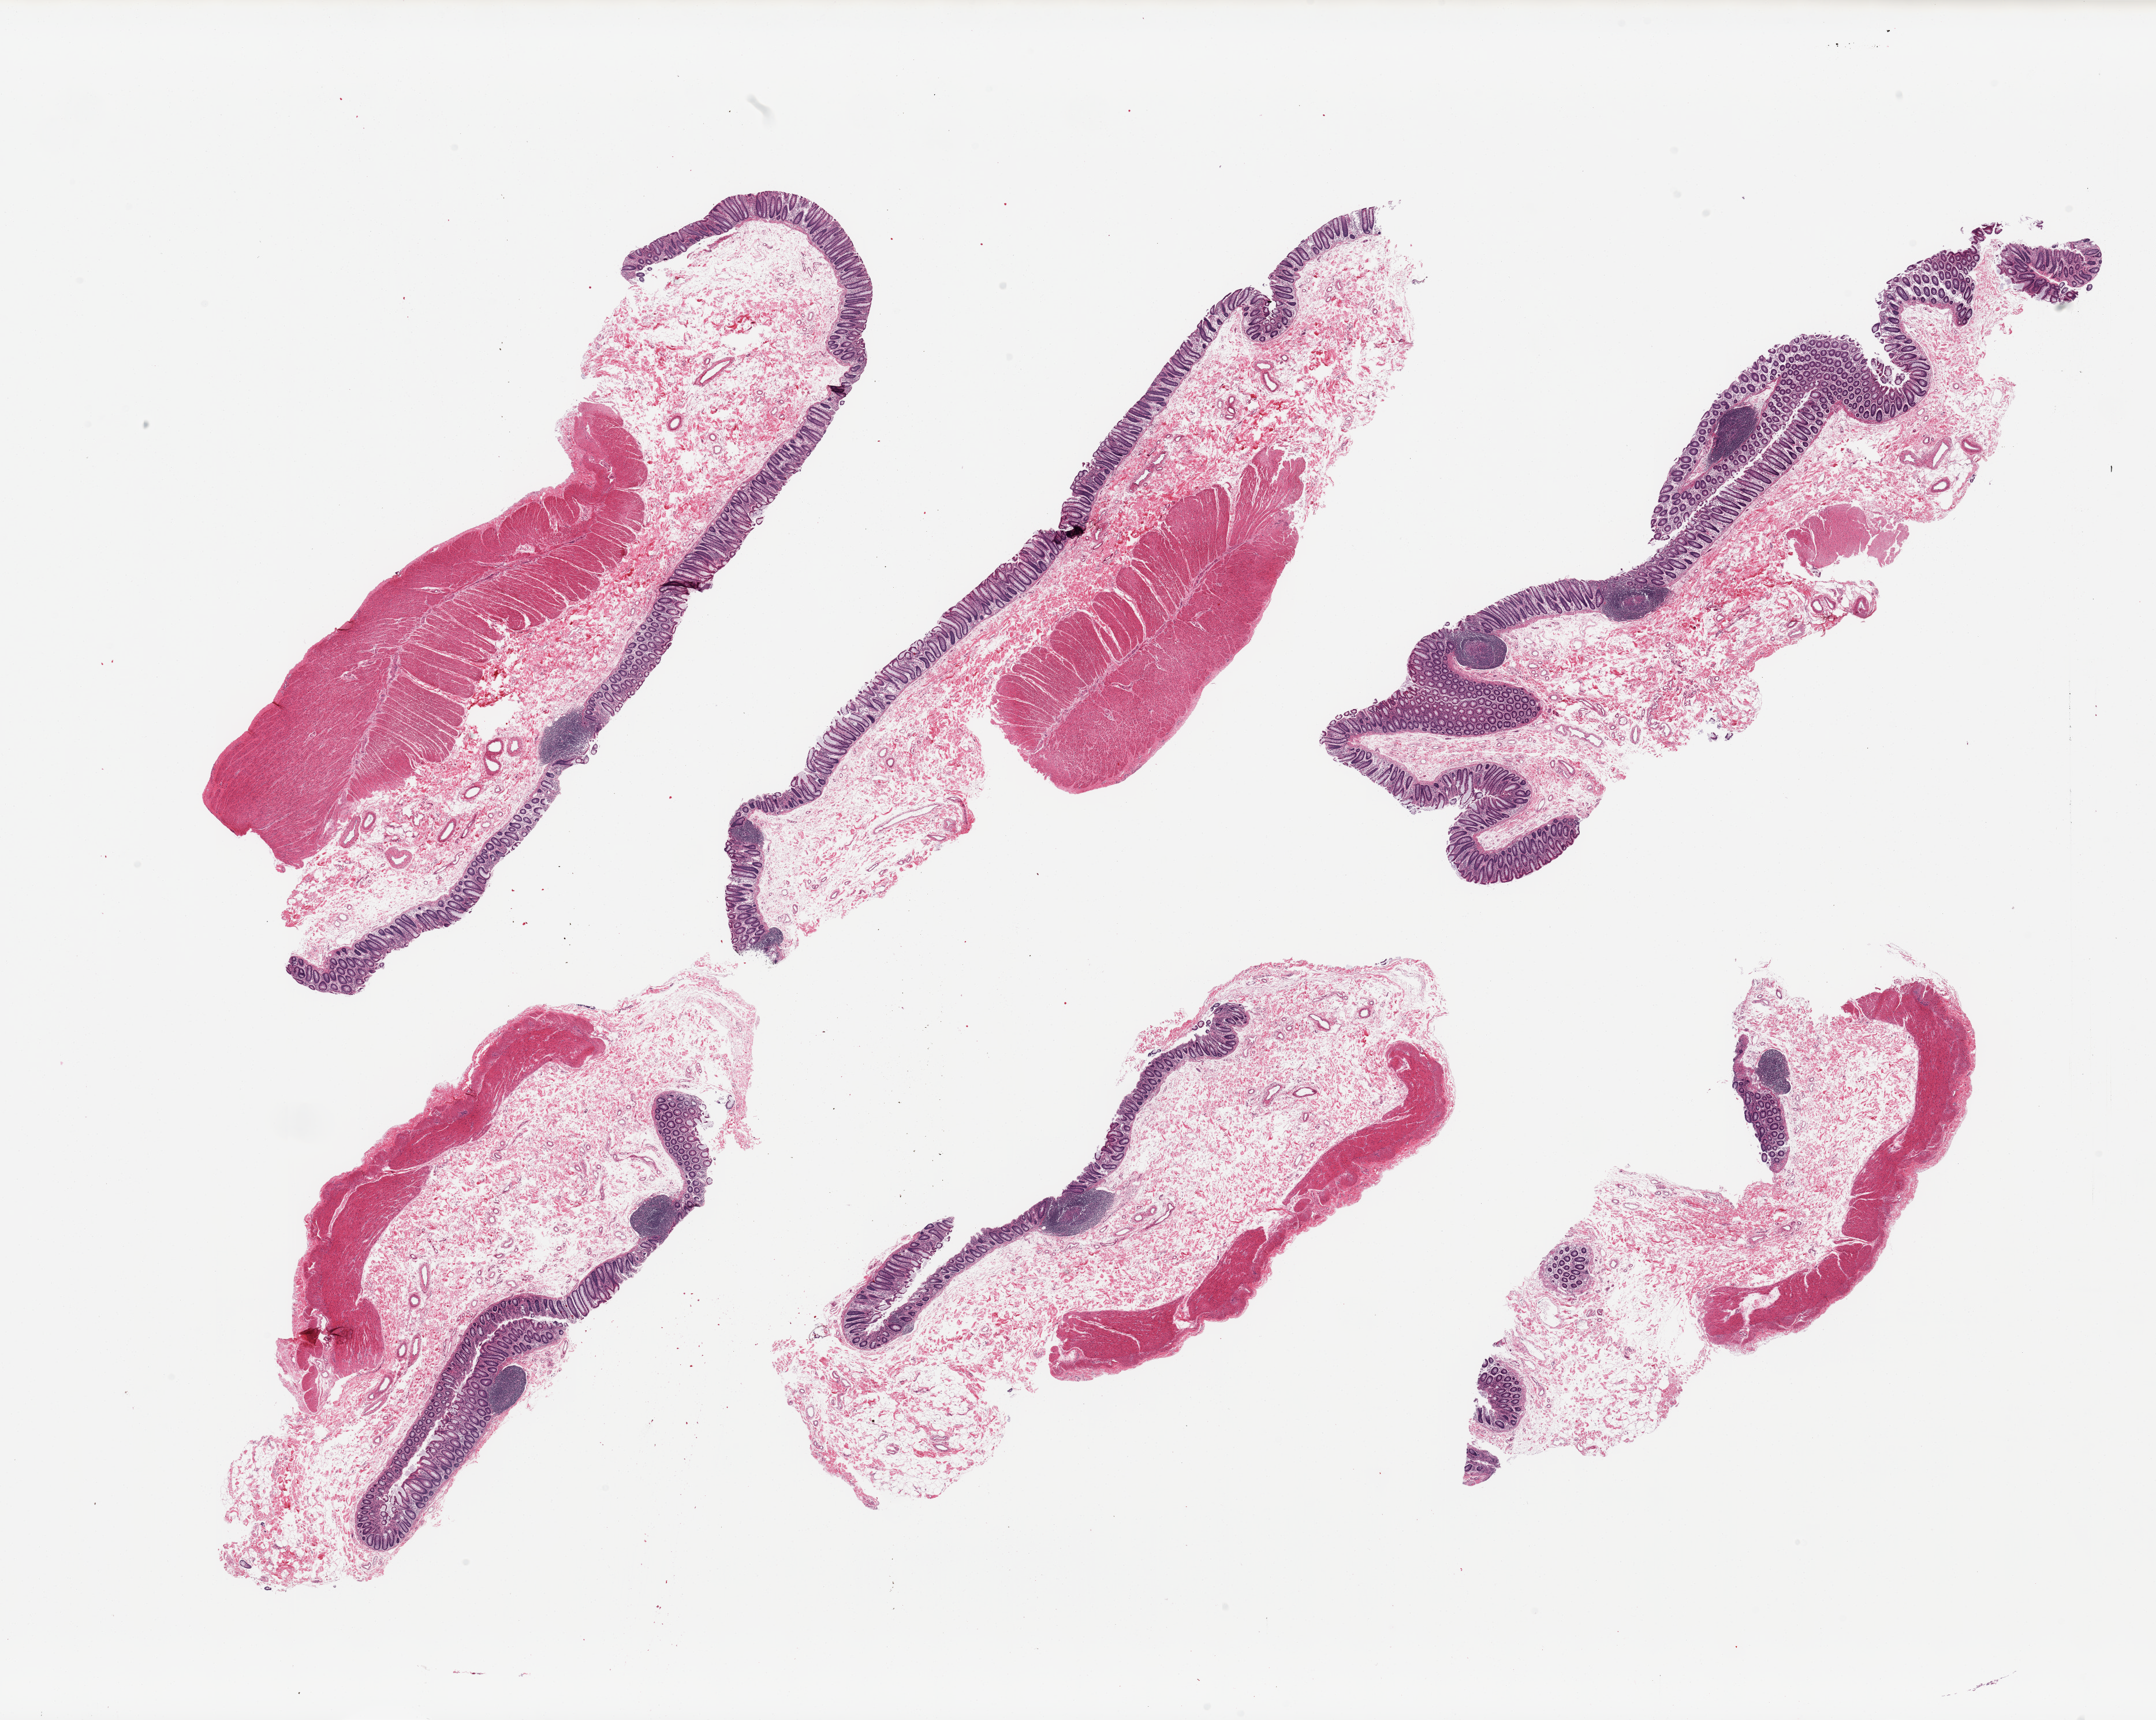
Haematoxylin and eosin whole-slide image, brightfield, whole scanned area (about 29.5 x 23.6 mm, acquisition: 20x scan) shown as a low-resolution overview, PAXgene-fixed, paraffin-embedded tissue, section of sigmoid colon (target tissue), donor tissue sample. Male donor.
Review note (as recorded): 6 pieces; all full thickness (with mucosa) rather than muscularis only.